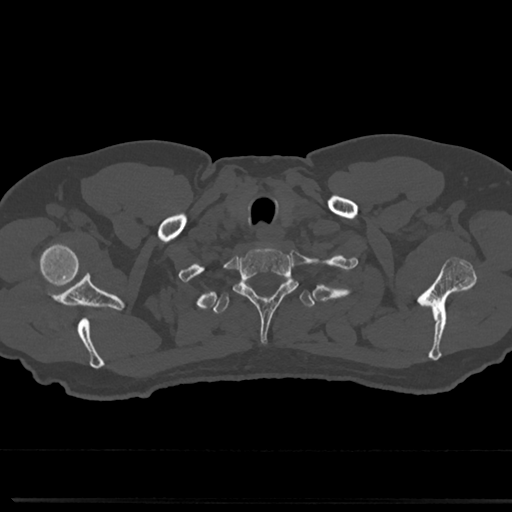
CT including the spine, one axial slice; position 665 of 817 along the scan axis; reconstruction kernel Br40s/3; 120 kVp; bone window (W 1800 / L 400 HU); 0.5 mm slice thickness; 512 × 512 image matrix, field of view 355 × 355 mm. Patient: male, 61 years. From the clinical record (not read from this slice): primary cancer: prostate.
Annotated regions visible in this slice (semi-automatically segmented with operator editing):
- T1 vertebra: bounding box (x1, y1, x2, y2) in pixels: (234, 247, 297, 341)
- T2 vertebra: (212, 277, 315, 315)